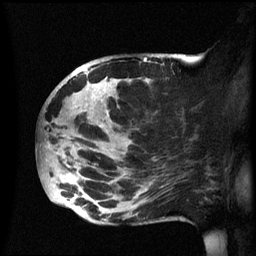
Breast MRI (dynamic contrast-enhanced), one sagittal slice. Slice 29 of 60 in the series (ordered by position). Dynamic contrast-enhanced series, image 2 of 3 at this slice position (ordered by acquisition). 1.5 T. TE 4.2 ms, TR 8.4 ms. 2.4 mm slice thickness. 256 × 256 image matrix, field of view 230 × 230 mm. Female patient, age 49 years.
Outlined on this slice (semi-automatic segmentation, software-assisted and operator-edited):
- analysis volume of interest (the breast-tissue region the enhancement analysis was run in; not a lesion): bounding box <39,54,174,225> (left, top, right, bottom; pixels)
- tumour enhancement mask (voxels above the 70 % enhancement threshold inside the analysis volume of interest): <66,59,149,213>